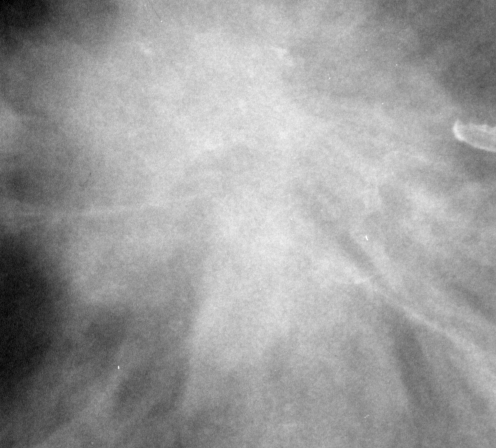
Cropped region of a digitized screen-film mammogram centred on a radiologist-marked abnormality; left breast; CC view.
Marked abnormality: mass, shape round, margins spiculated; BI-RADS assessment category 5; pathology result (as recorded, not read from the image): malignant.